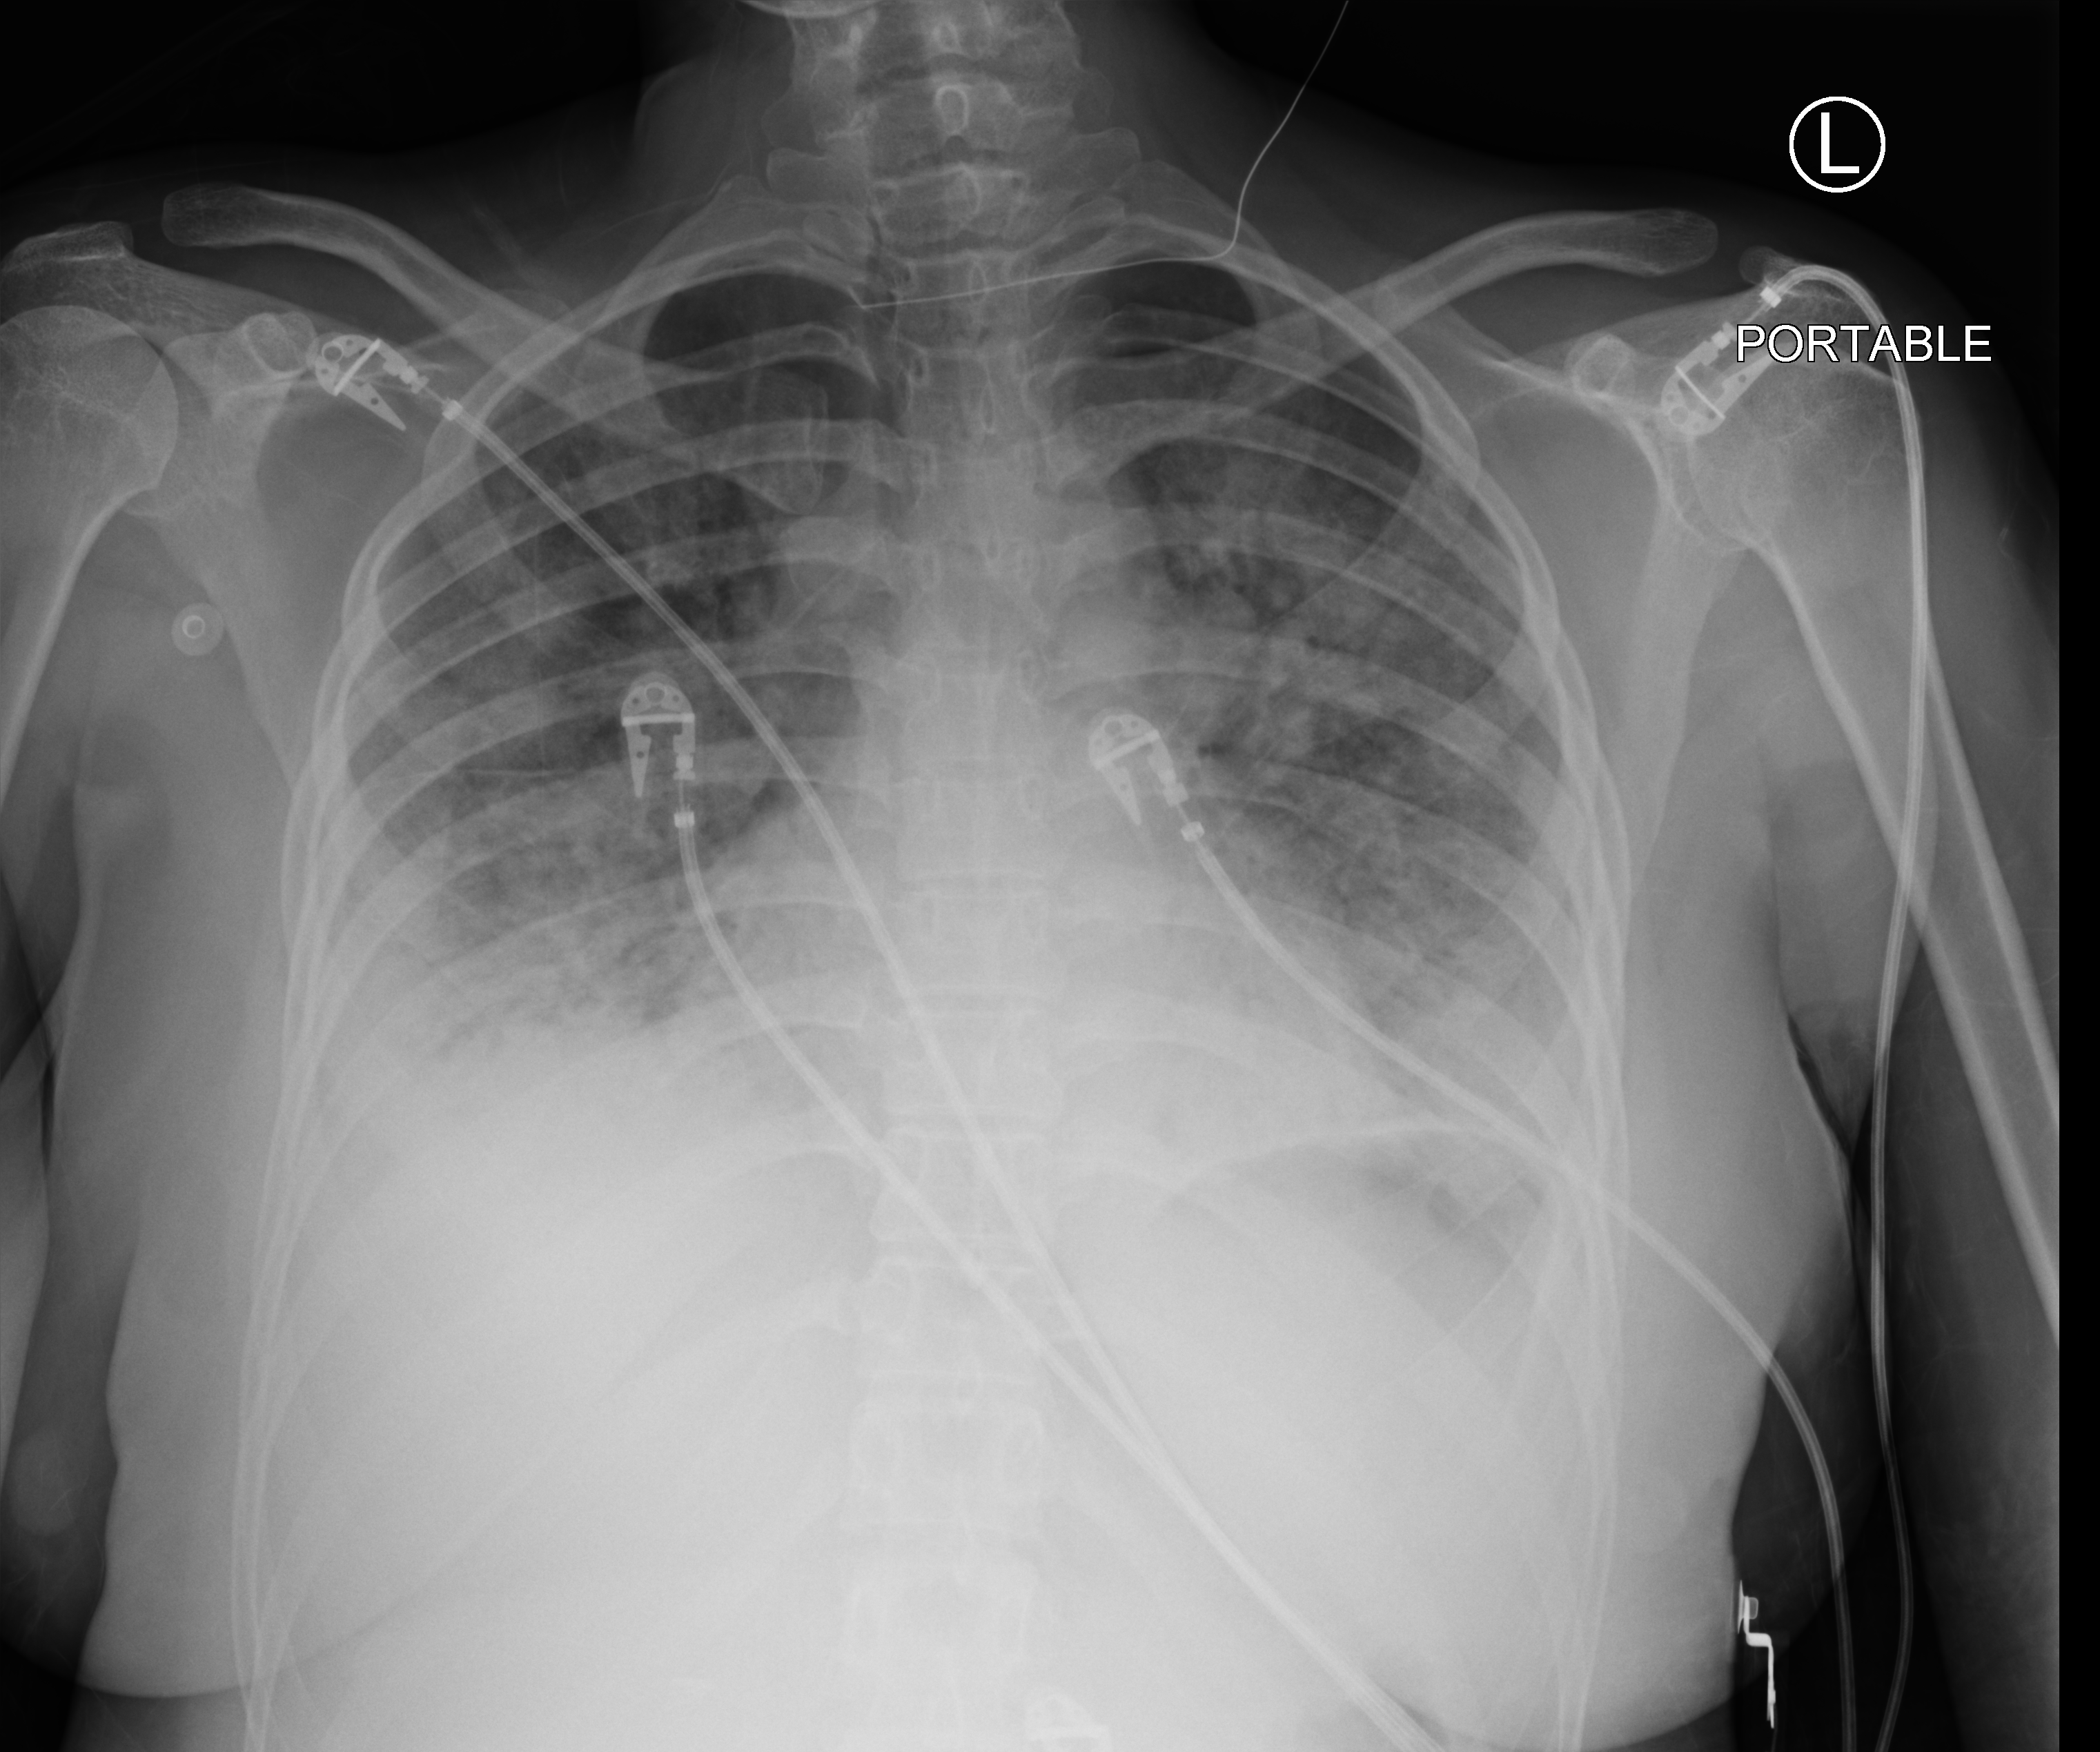
Bedside chest radiograph (computed radiography); anteroposterior (AP) projection. Adult patient hospitalised with COVID-19, age 18–59 years.
Admission-level facts for this patient (not findings on this image; timing relative to this image not recorded):
- mechanically ventilated during this hospital stay: yes
- admitted to intensive care during this hospital stay: yes